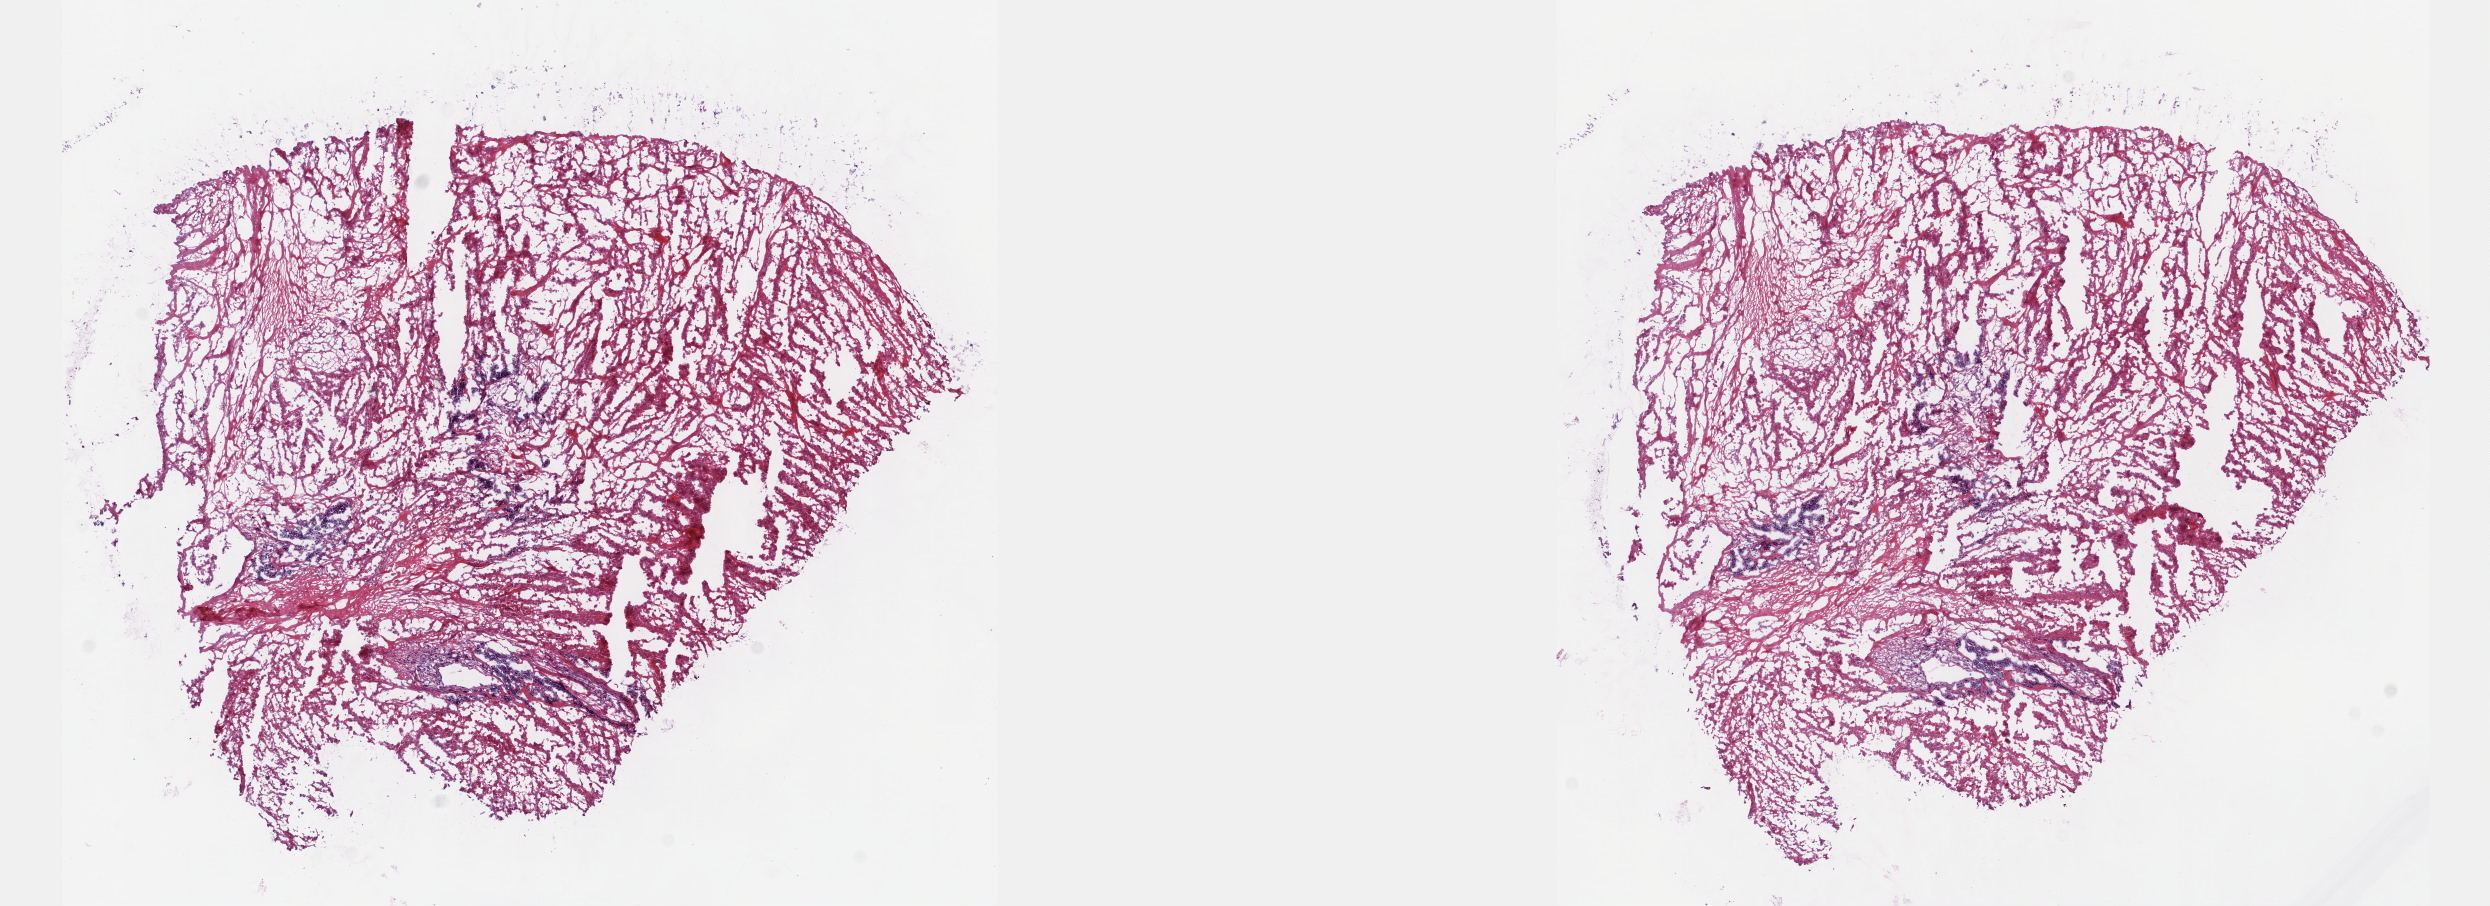
H&E whole-slide image, a low-resolution overview of the entire scanned area, about 20.1 x 7.3 mm. Formalin-fixed paraffin-embedded (FFPE) diagnostic section. Sample: primary tumour, breast. Female, age 29 years at initial diagnosis.
Pathologic diagnosis: Infiltrating duct carcinoma, NOS.